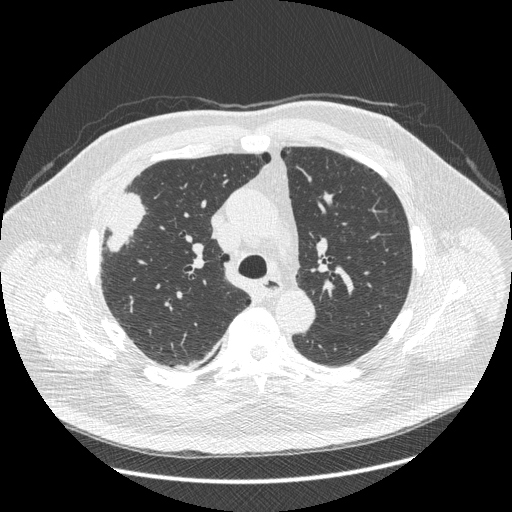
Low-dose screening chest CT, one axial slice; position 290 of 426 along the scan axis; reconstruction kernel STANDARD; 120 kVp; lung window (W 1500 / L -600 HU); 1.25 mm slice thickness; 512 × 512 image matrix.
Outlined on this slice (outlined manually by an expert reader):
- lesion 1 (tumor, upper lobe of right lung): bounding box (x1, y1, x2, y2) in pixels: (107, 193, 145, 251)